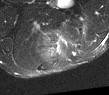
MRI of an extremity soft-tissue mass, one axial slice; position 39 of 52 along the scan axis; T2-weighted fat-saturated; MR volume resampled by the dataset authors to the PET/CT grid (not the native acquisition matrix); 3.27 mm slice thickness; 109 × 95 image matrix, field of view 106 × 93 mm. Male patient. Case-level facts recorded for this patient, not image findings: histological type: synovial sarcoma; site of the primary tumour: left poplietal fossa.
Outlined on this slice (expert contour drawn on MRI and transferred to this co-registered scan by the dataset authors):
- gross tumour volume (mass): bounding box (x1, y1, x2, y2) in pixels: (40, 31, 62, 55)